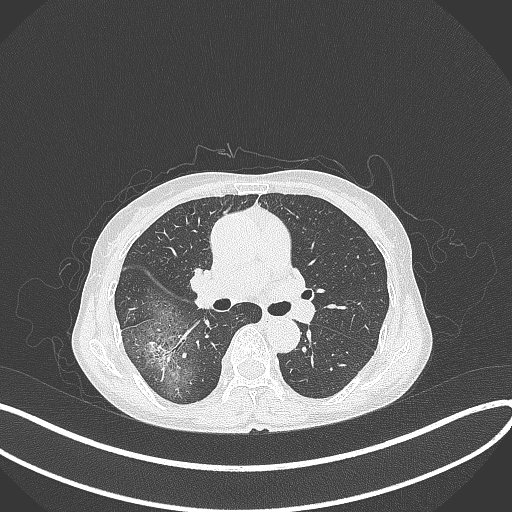
Chest CT, one axial slice; position 231 of 371 along the scan axis; reconstruction kernel B70f; 120 kVp; lung window (W 1500 / L -600 HU); 512 × 512 image matrix. Female patient, age 69 years. Case-level facts recorded for this patient, not image findings: clinical TNM (as recorded): T1b N0 M0; histopathological grade: G2-3.
Structures marked on this image (rectangle marked by the reading radiologist):
- lung tumour (recorded histology: adenocarcinoma): box from (x=139, y=334) to (x=176, y=384) px